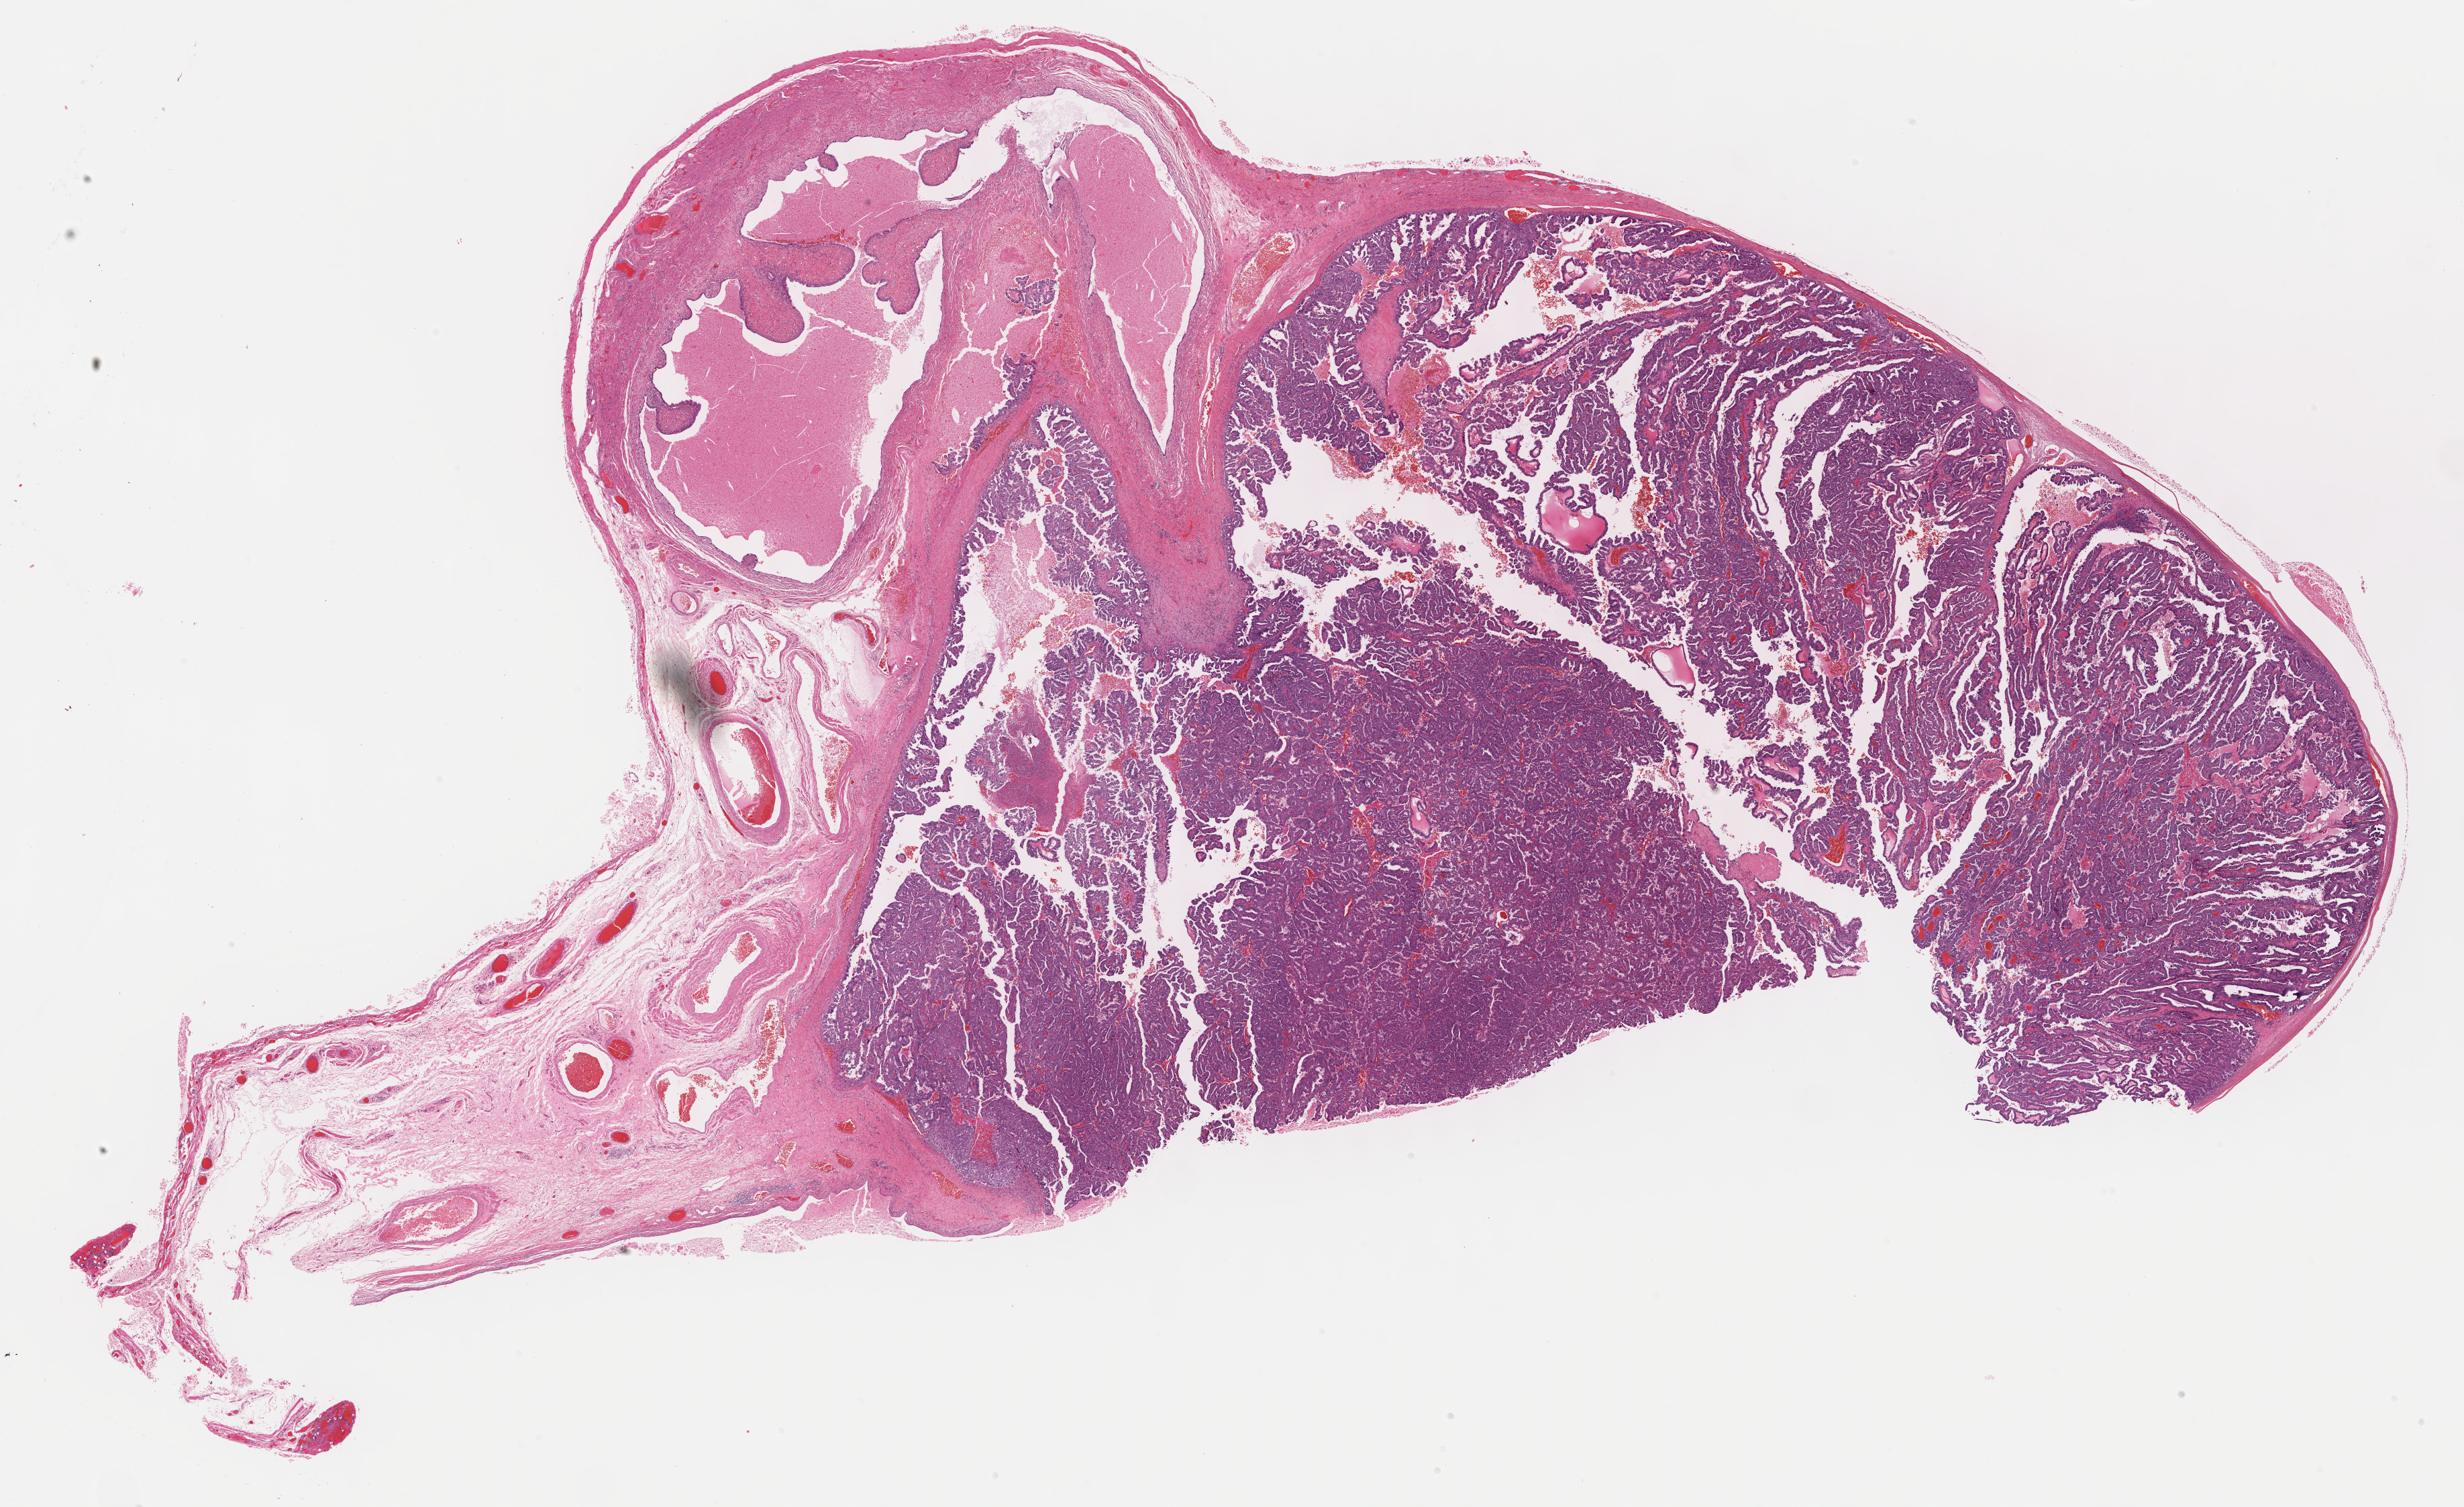
Digitized Hematoxylin and eosin (H&E) stained tissue section (whole slide), whole scanned area (about 29.7 x 18.2 mm, slide scanned at 40x) shown as a low-resolution overview. Formalin-fixed paraffin-embedded (FFPE) diagnostic section. Primary tumour sample from the ovary. Female, age 73 years at initial diagnosis. Histologic grade: G3 (poorly differentiated).
* FIGO stage: IV
* histologic diagnosis: Serous cystadenocarcinoma, NOS